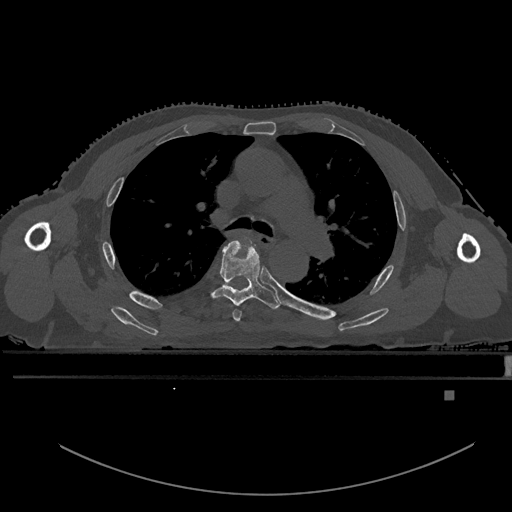
CT including the spine, one axial slice. Position 365 of 969 along the scan axis. Bone window (W 1800 / L 400 HU). 0.5 mm slice thickness. 512 × 512 image matrix, field of view 456 × 456 mm. Male patient, age 82 years. Case-level facts recorded for this patient, not image findings: primary cancer: prostate; vertebrae with lytic lesions (as recorded): T11, T9, T8, T2.
Annotated regions visible in this slice (semi-automatic segmentation, software-assisted and operator-edited):
- T4 vertebra: box from (x=233, y=239) to (x=251, y=322) px
- T5 vertebra: (x=202, y=240)–(x=280, y=309)